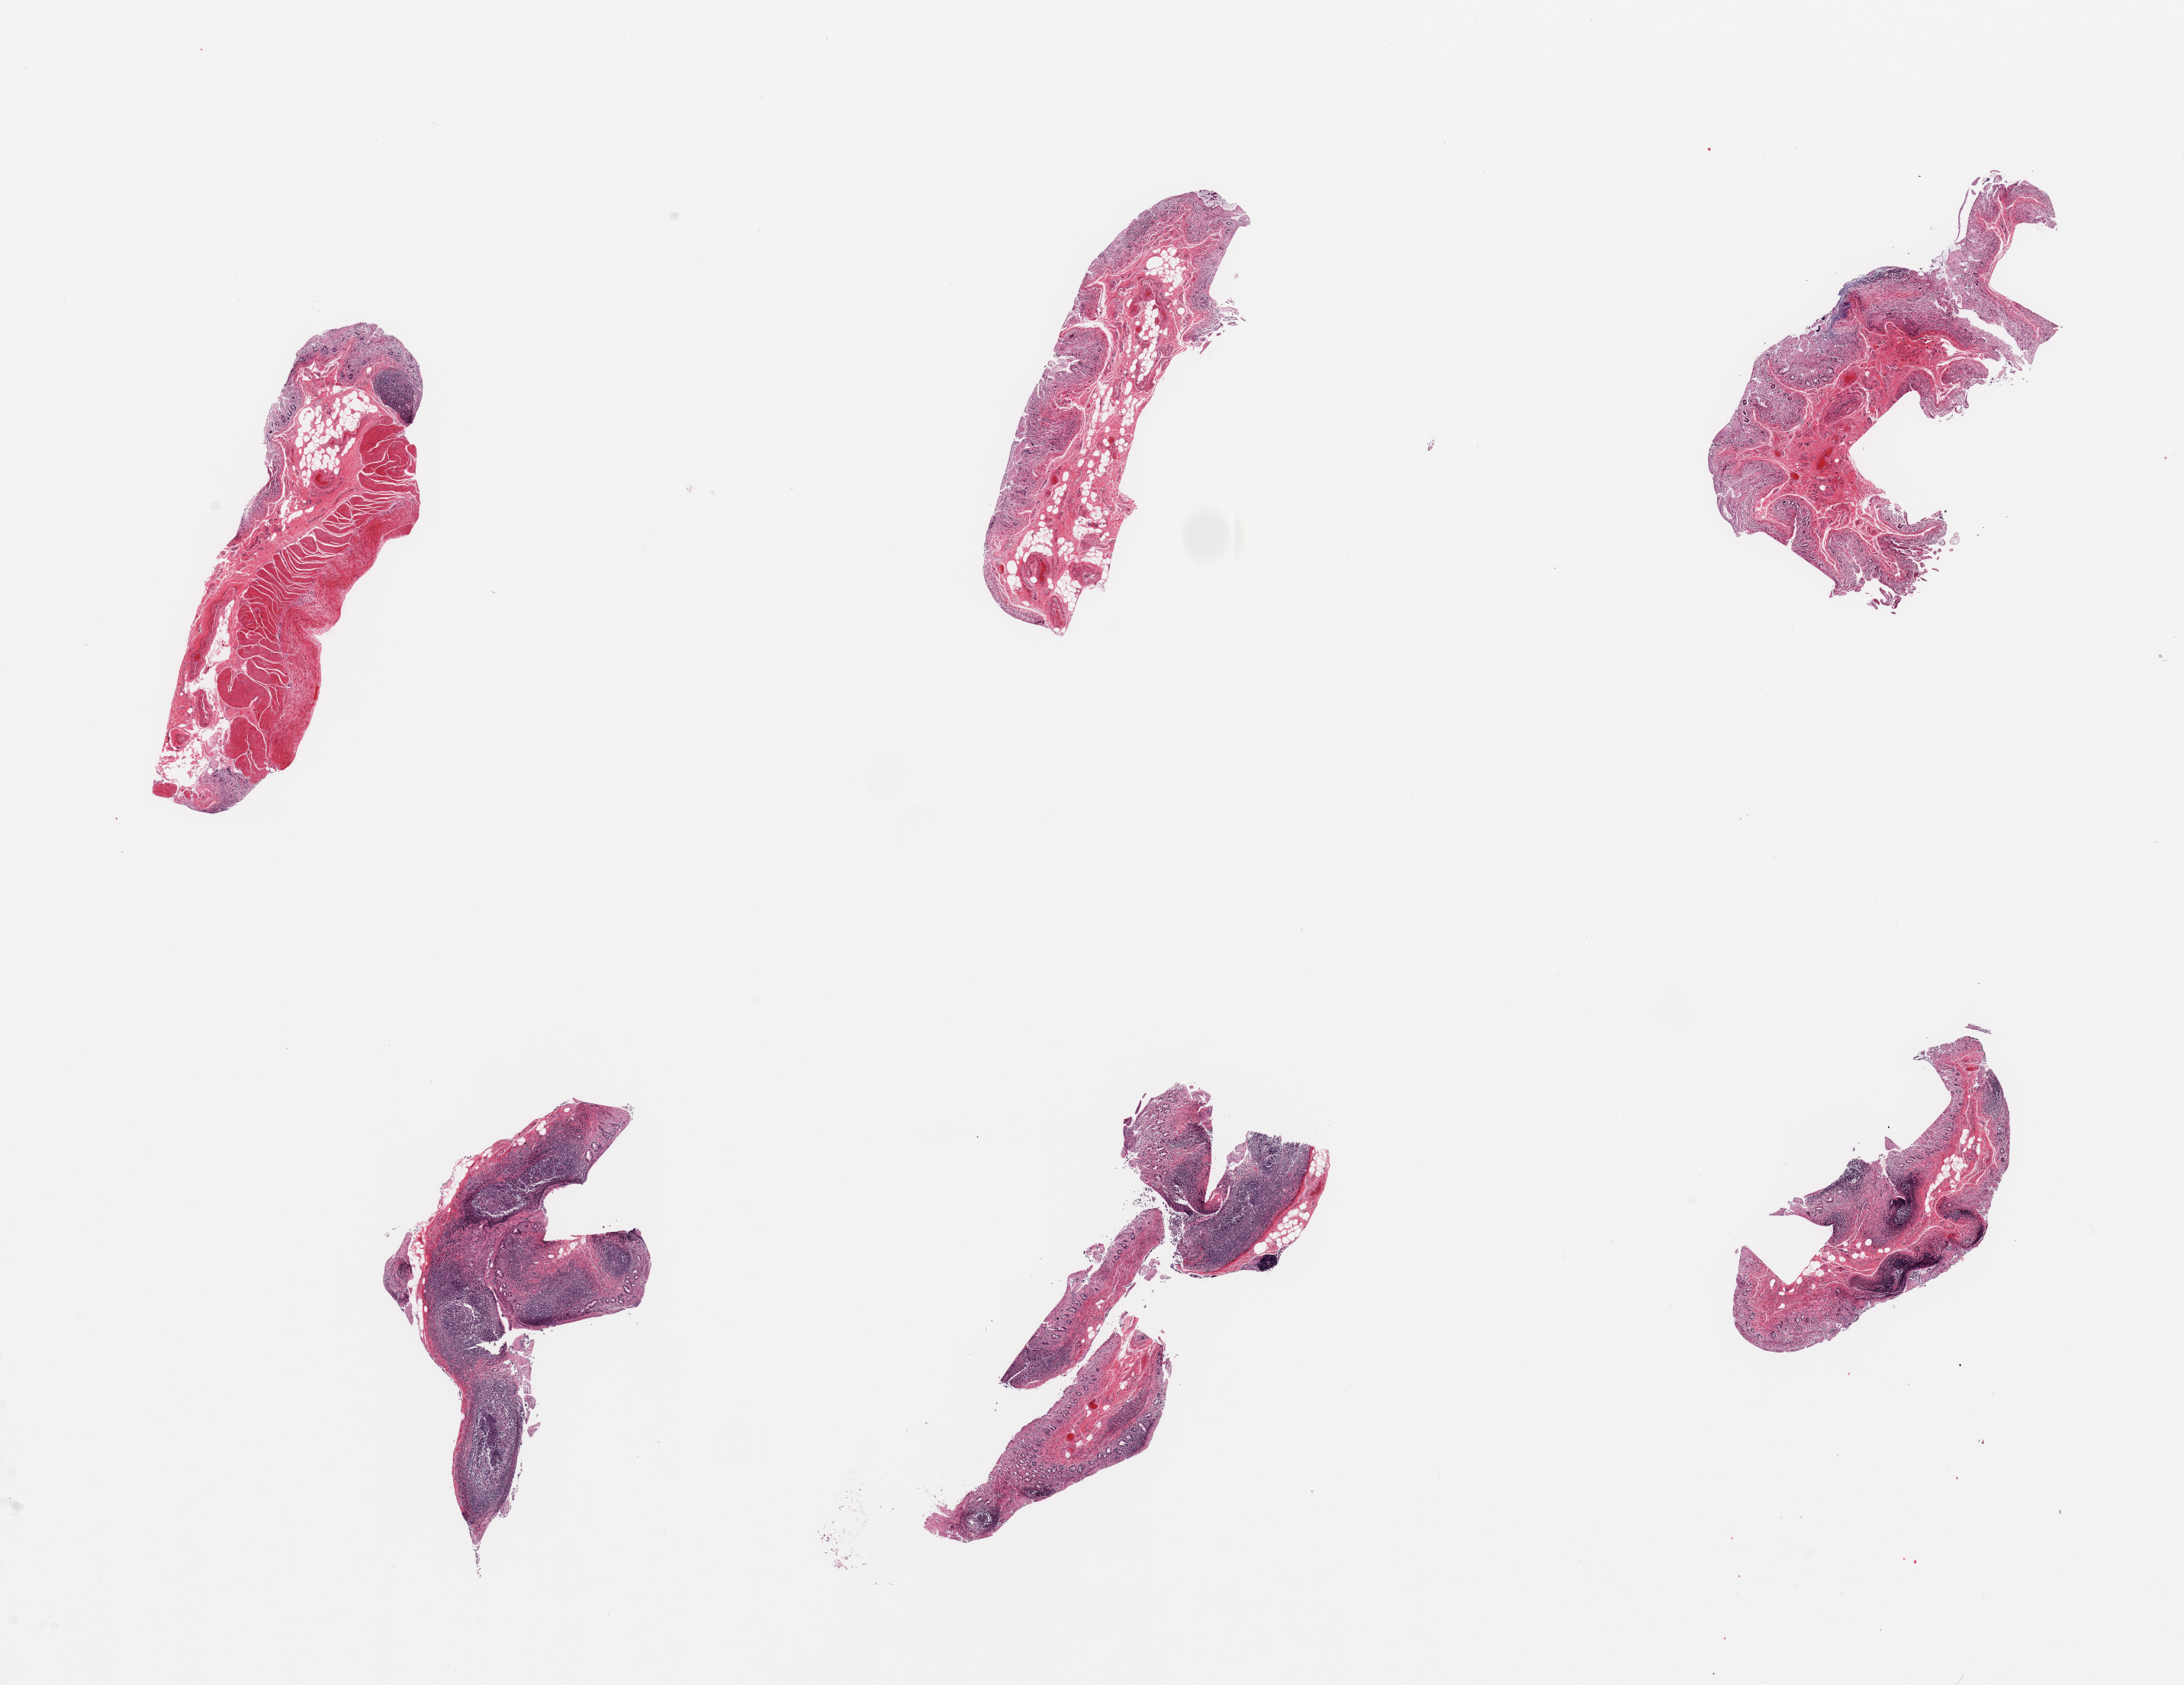
Whole-slide image, hematoxylin and eosin (H&E) stain, a low-resolution overview of the entire scanned area, about 22.6 x 17.5 mm, PAXgene-fixed, paraffin-embedded tissue, section of ileum (target tissue), donor tissue sample. Male donor.
- review note (as recorded): 6 pieces, well preserved target lymphoid aggregates are ~30% pf tissue